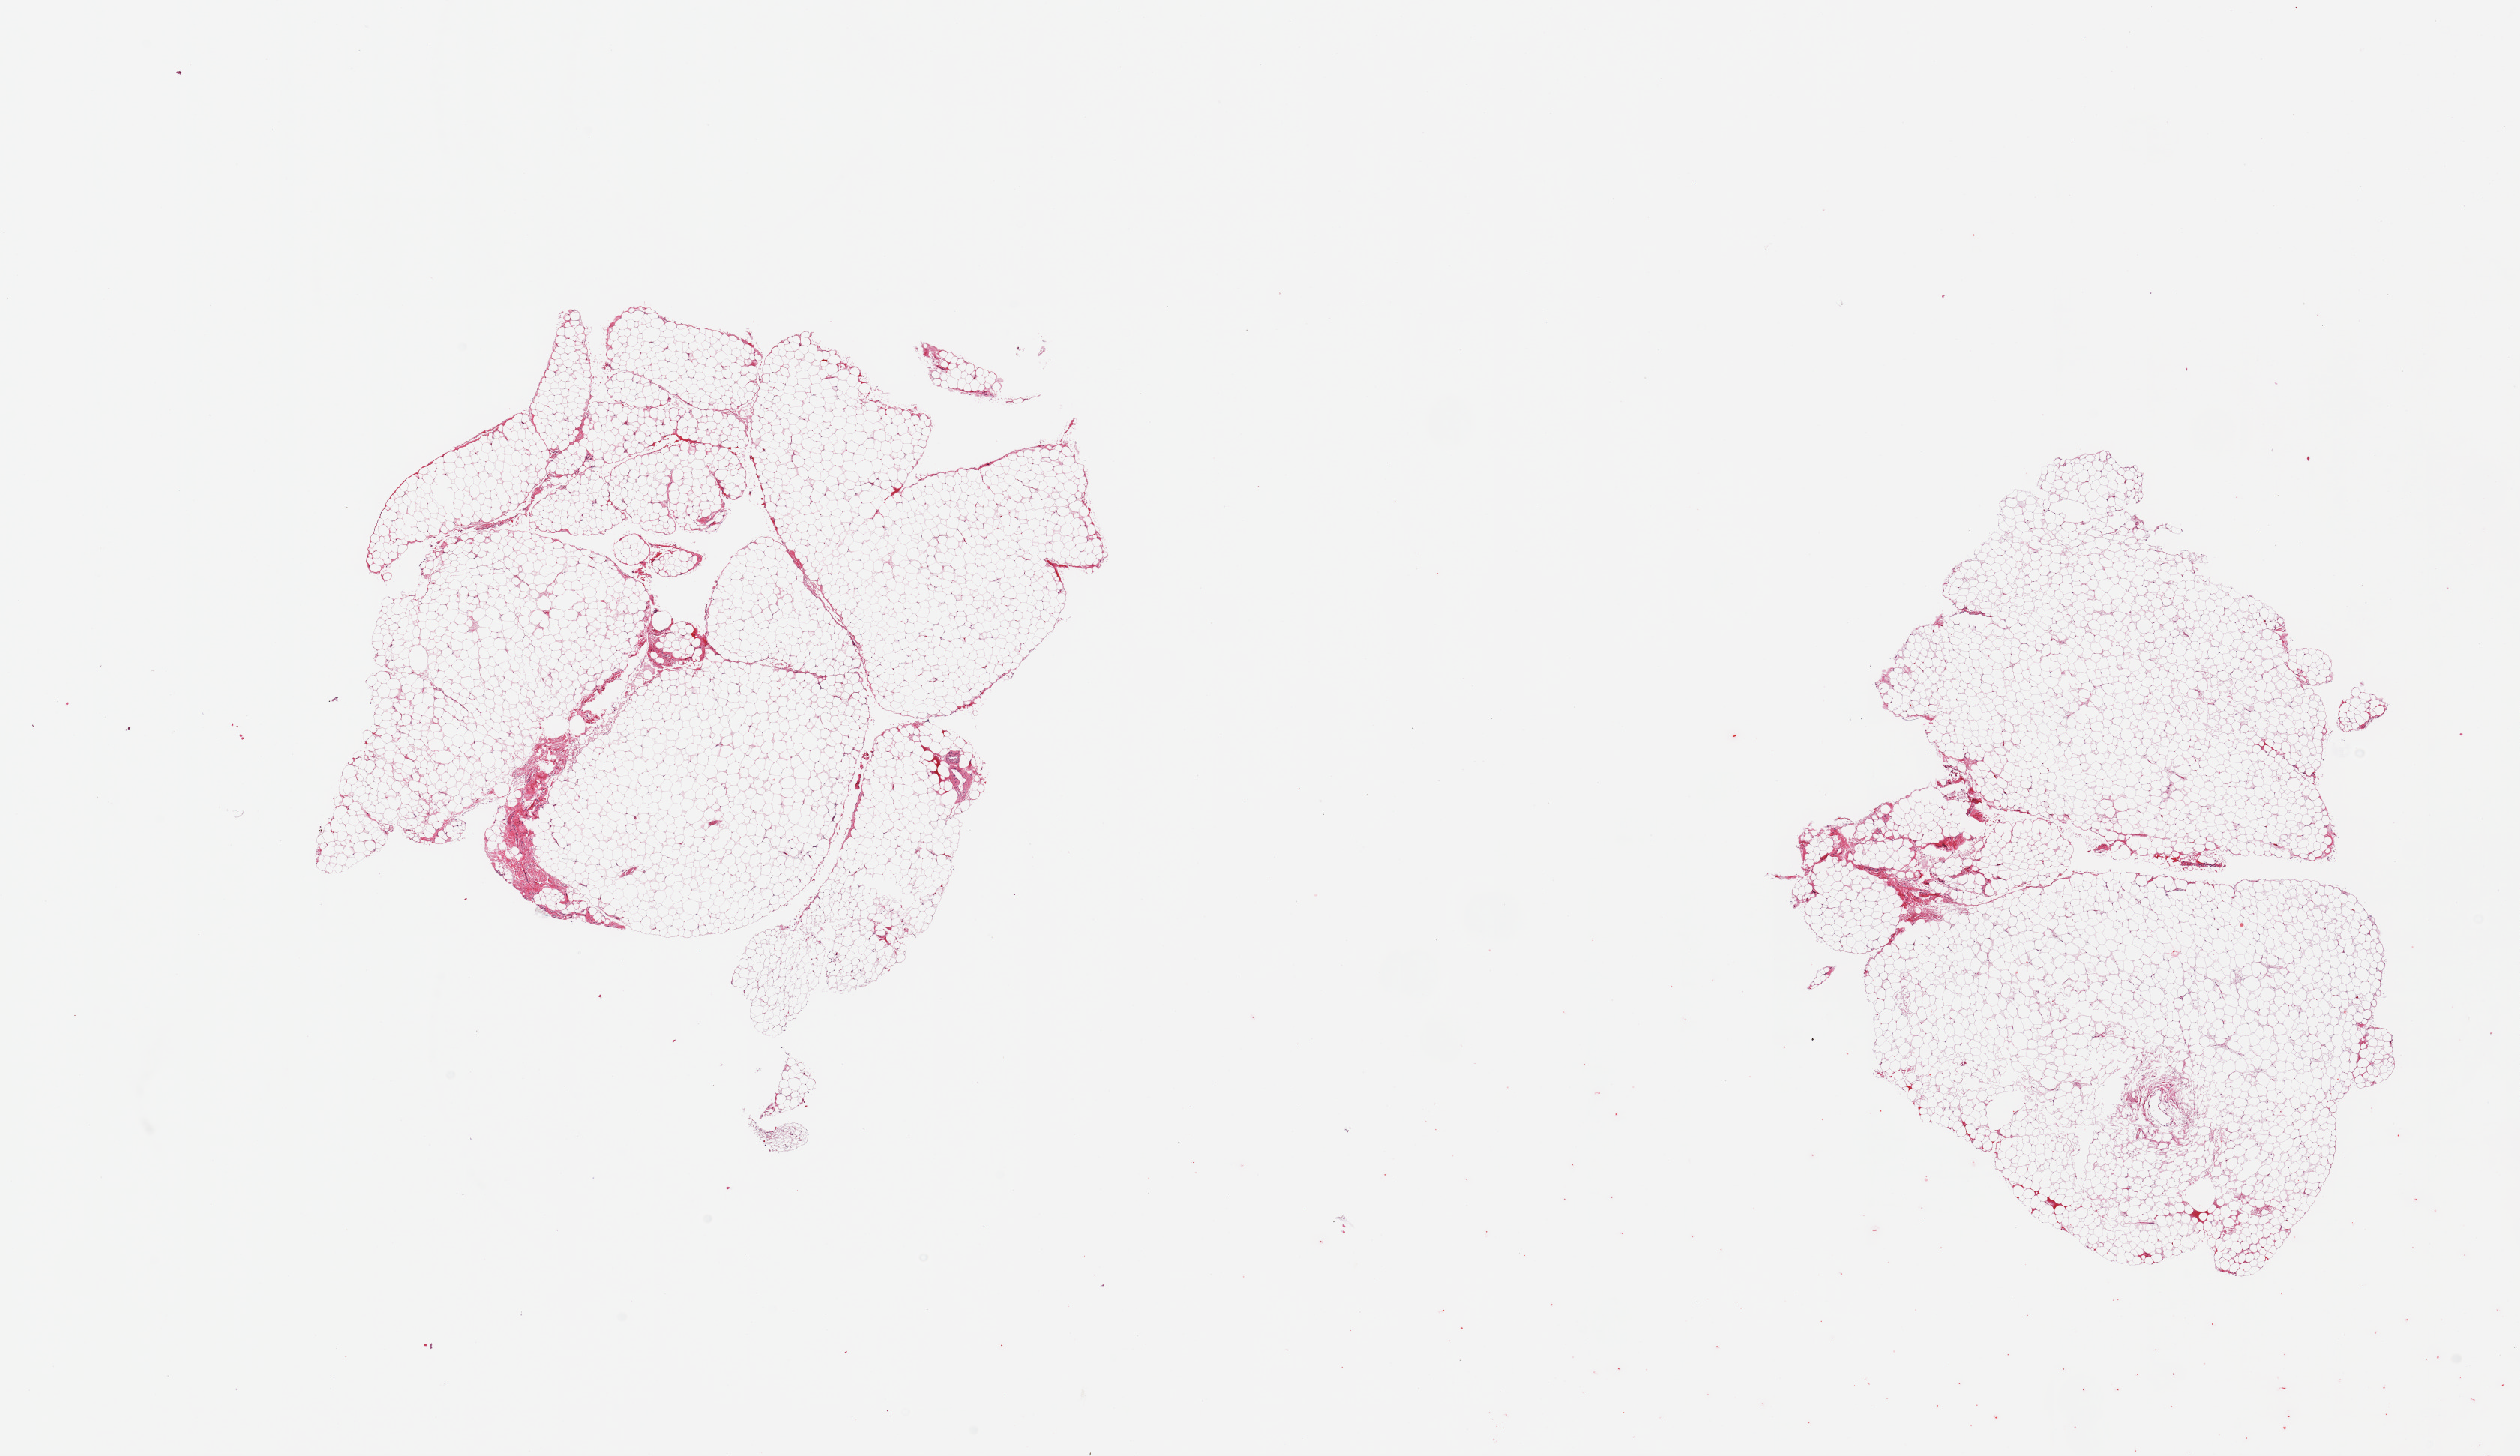
Hematoxylin and eosin (H&E) whole-slide image, brightfield — whole scanned area (about 26.6 x 15.4 mm, from a 20x scan) shown as a low-resolution overview; PAXgene-fixed, paraffin-embedded tissue; section of omentum (target tissue); donor tissue sample. Donor sex: male.
• pathologist's review note for this sample: 2 pieces; 2% fibrous content